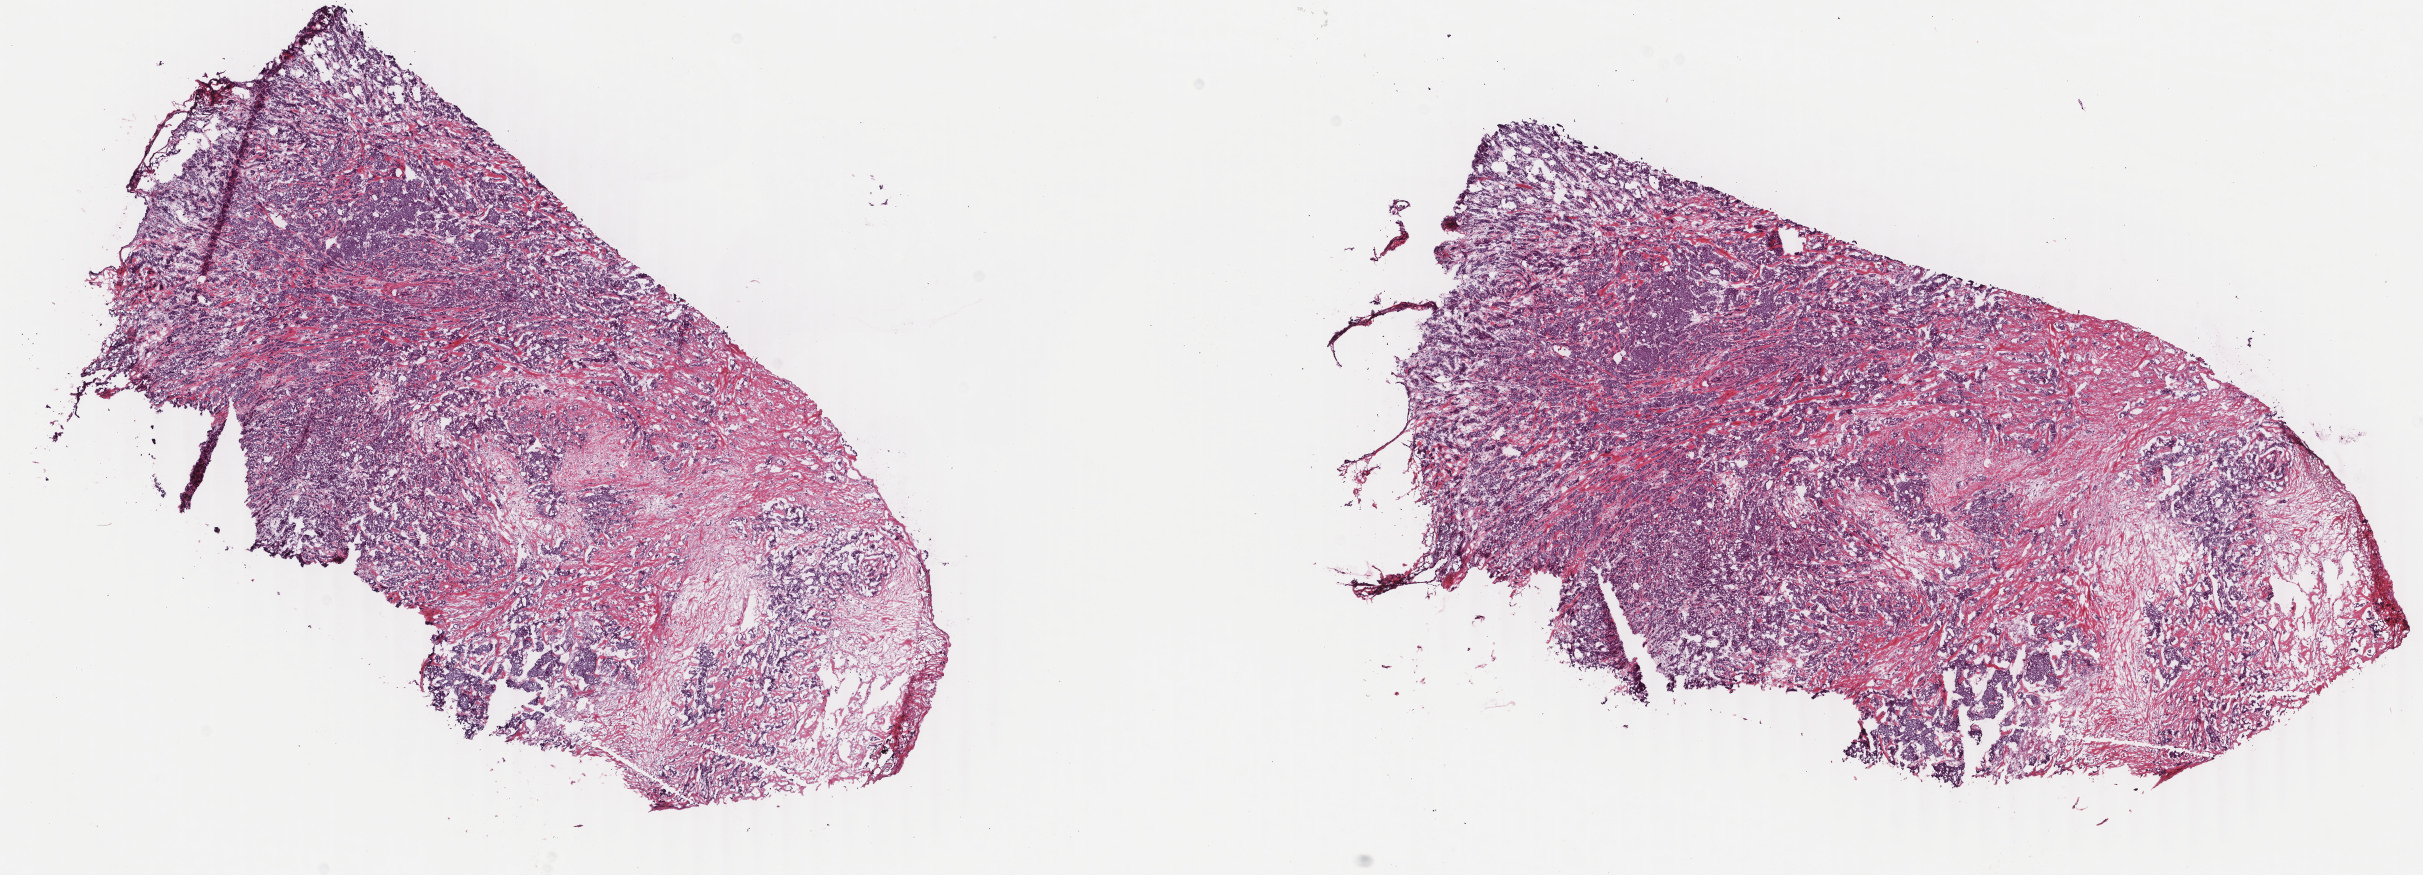
Digitized H&E tissue section (whole slide), whole scanned area (about 19.3 x 7.0 mm) shown as a low-resolution overview, frozen section from the top of the tissue portion, breast, primary tumour sample. Patient: female, age at initial diagnosis 55 years. Pathologist review of this section (percent, as recorded): tumour cells 85%, tumour nuclei 85%, normal cells 0%, stromal cells 15%, necrosis 0%. Infiltration values recorded for this section: lymphocyte infiltration 2%, monocyte infiltration 1%, neutrophil infiltration 0%.
AJCC pathologic stage: IIIA. Pathologic diagnosis: Infiltrating duct carcinoma, NOS. Lymph nodes positive (case pathology): 7 of 14 examined.